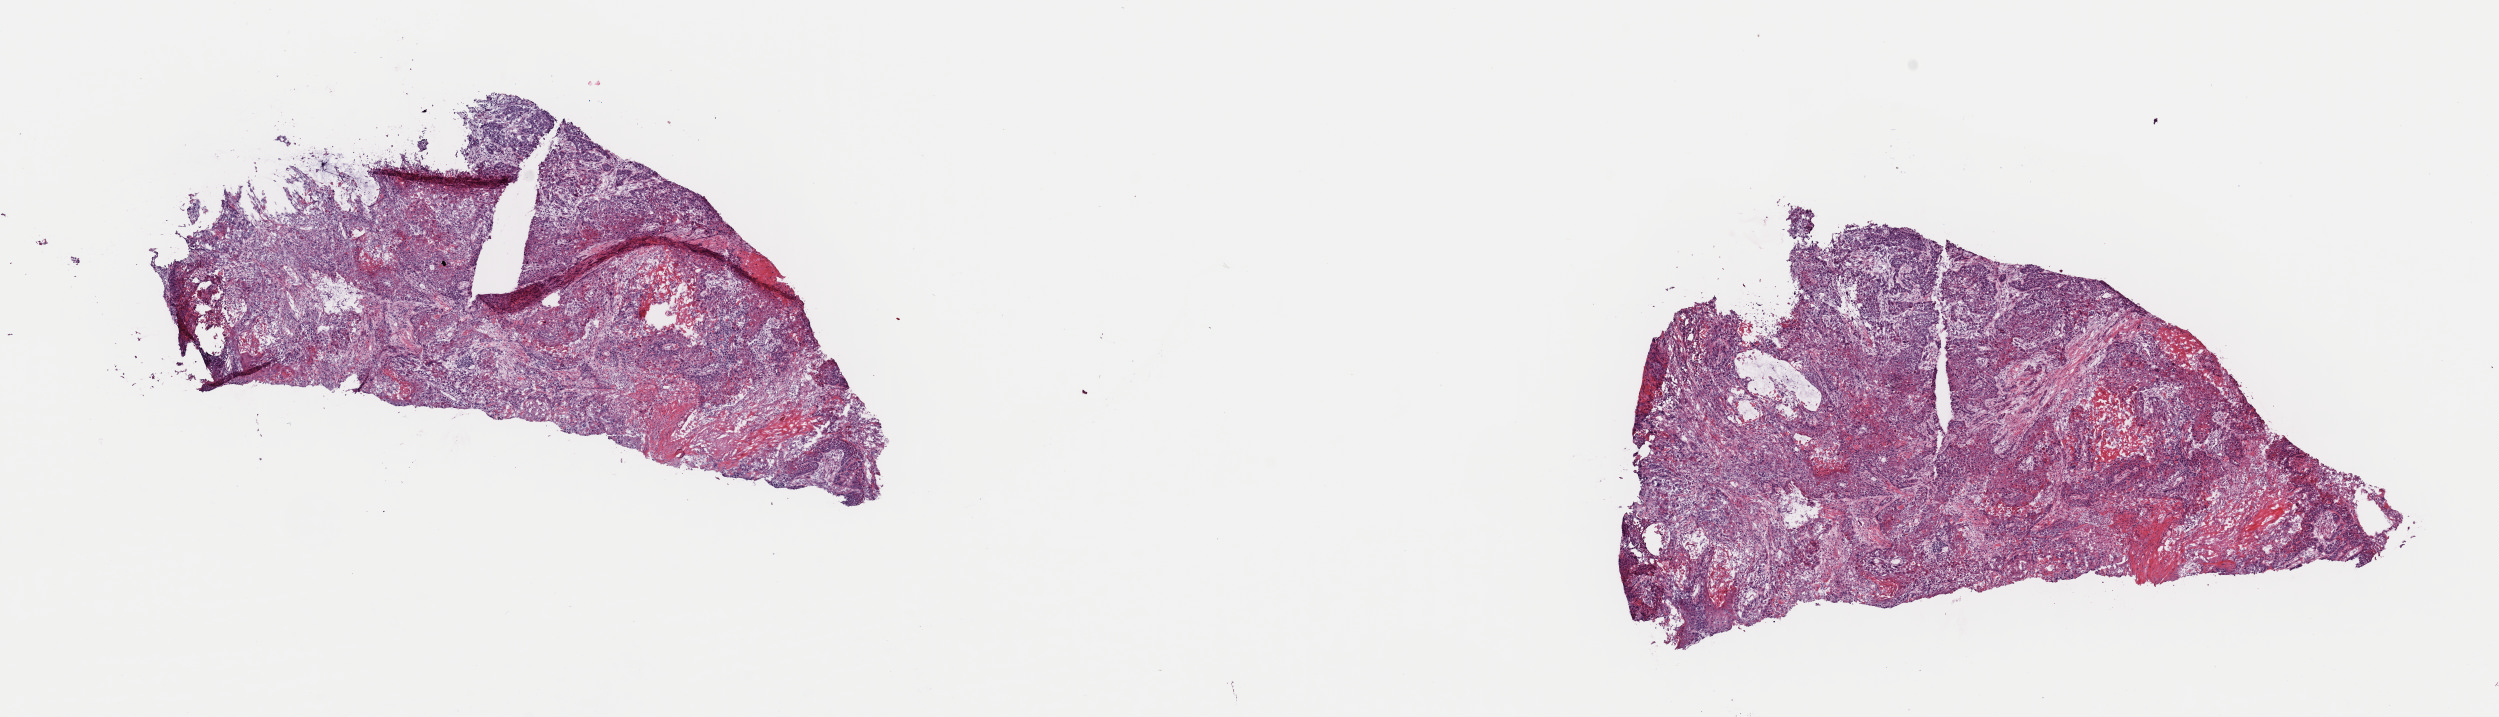
Whole-slide histology image, H&E-stained — low-resolution overview of the scanned area, about 19.7 x 5.7 mm; frozen section from the top of the tissue portion; sample: primary tumour, lung. Male, age 78 years at initial diagnosis. Pathologist review of this section (percent, as recorded): tumour cells 98%, tumour nuclei 75%.
Diagnosis: Squamous cell carcinoma, NOS (upper lobe, lung).